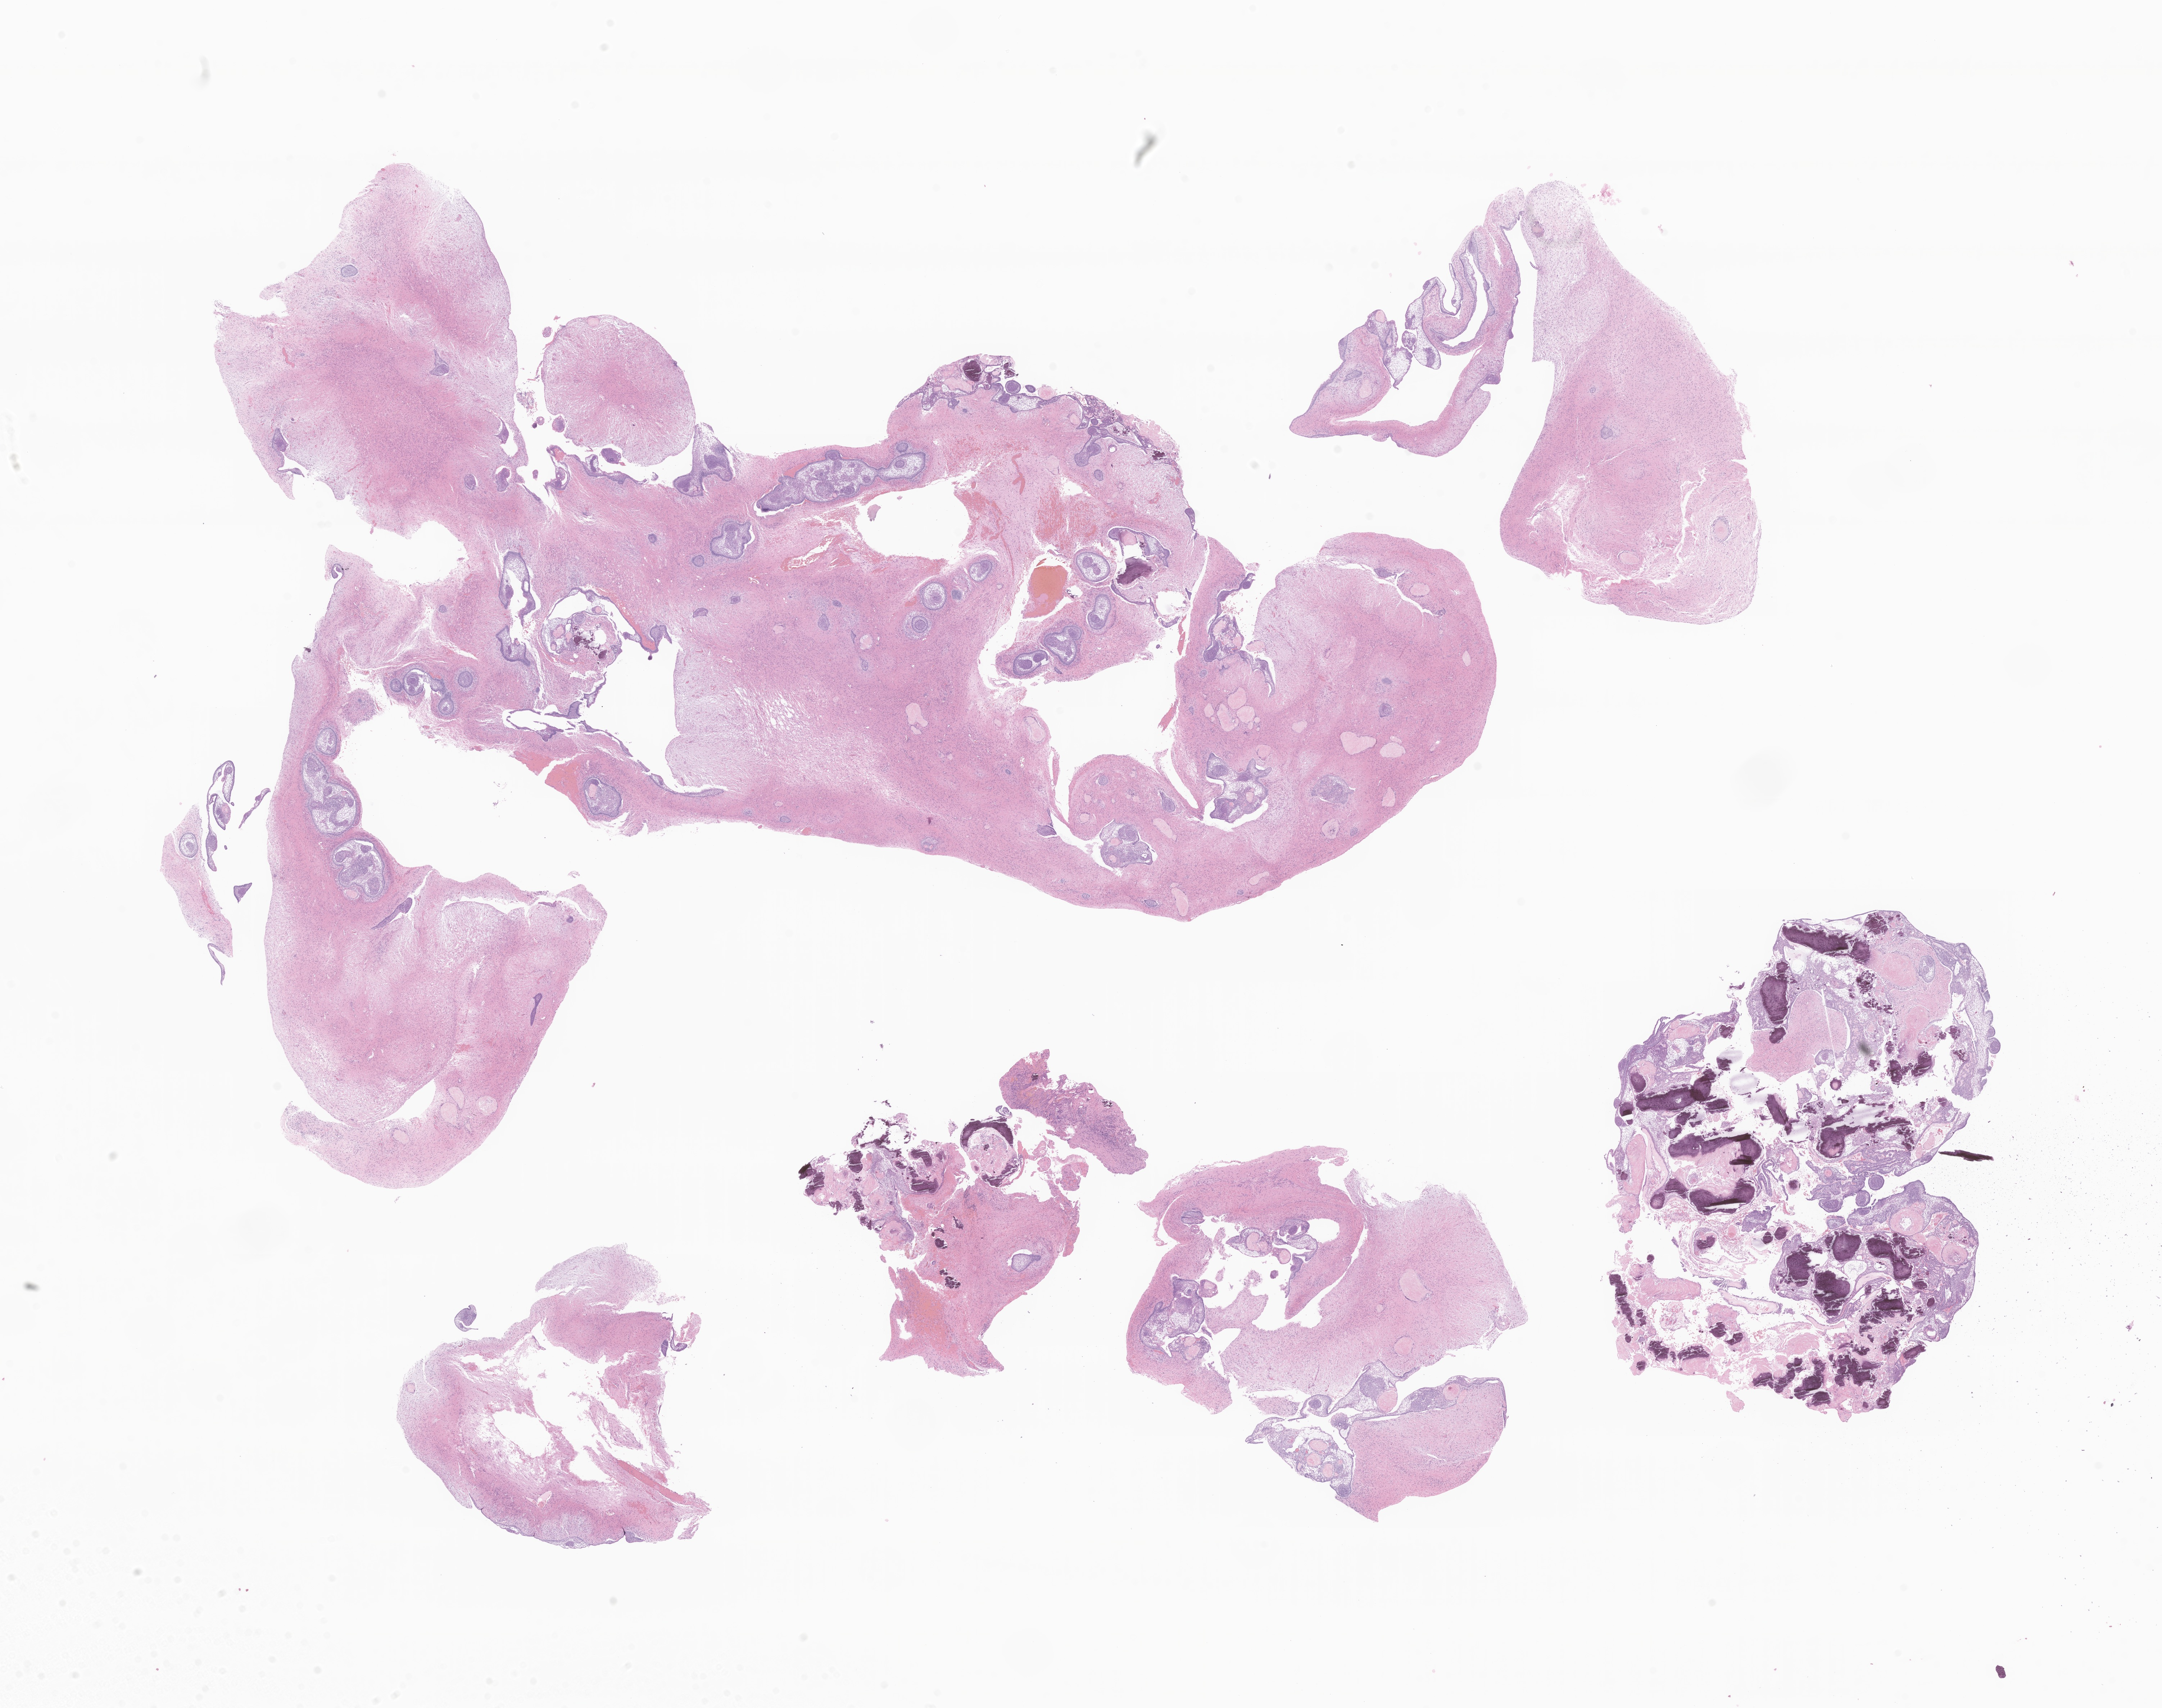
H&E whole-slide image of tumor tissue from the brain, low-resolution overview of the scanned area, about 25.3 x 20.0 mm. Formalin-fixed, paraffin-embedded (FFPE) tissue. Patient: female, age 133 months.
Diagnosis (ICD-O-3 morphology term): Craniopharyngioma, adamantinomatous.